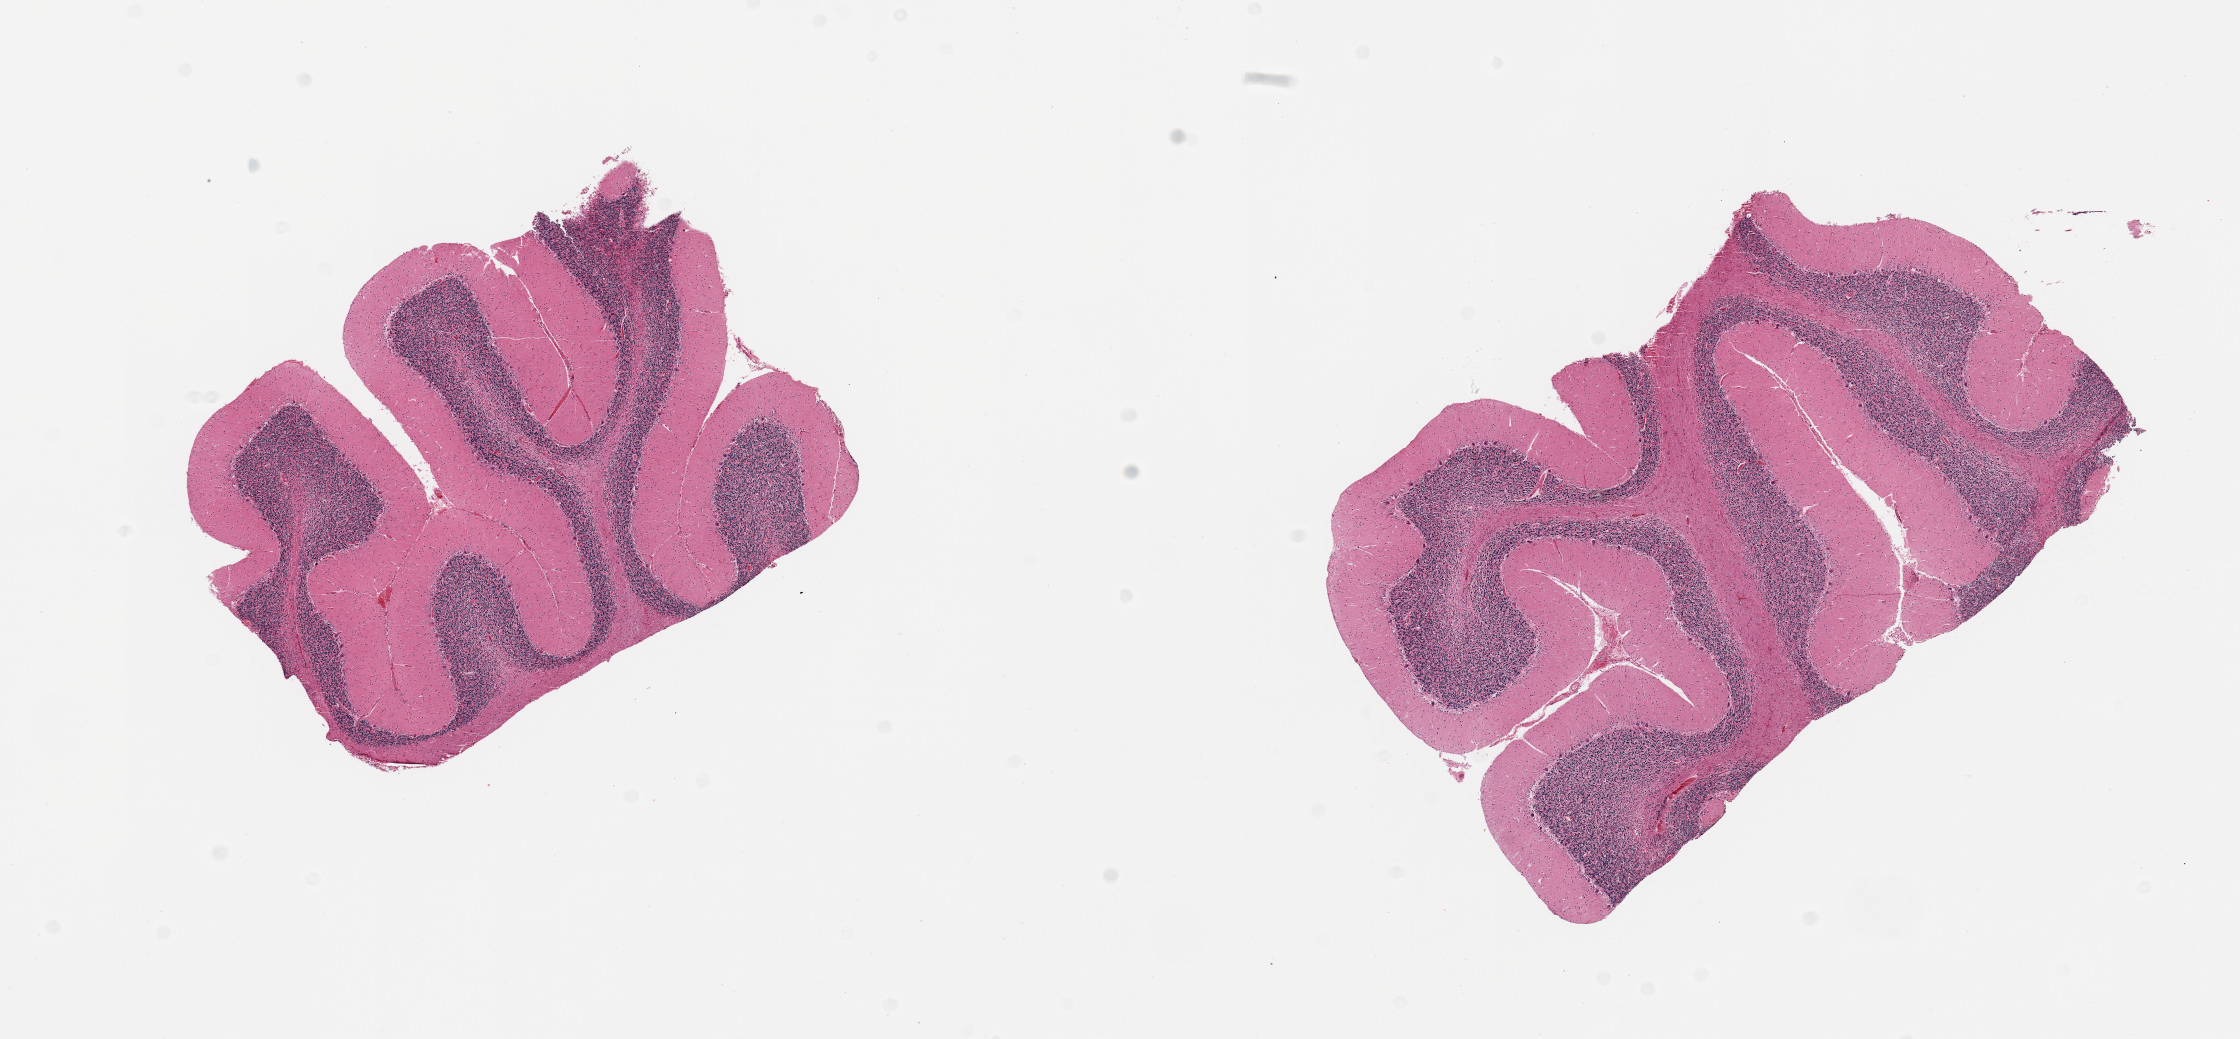
Hematoxylin and eosin (H&E) whole-slide image, low-resolution overview of the scanned area, about 17.7 x 8.2 mm; PAXgene-fixed, paraffin-embedded tissue; sampled site (target tissue): cerebellum; donor tissue sample. Male donor.
Pathologist's review note for this sample: 2 pieces; should have 4 pieces.